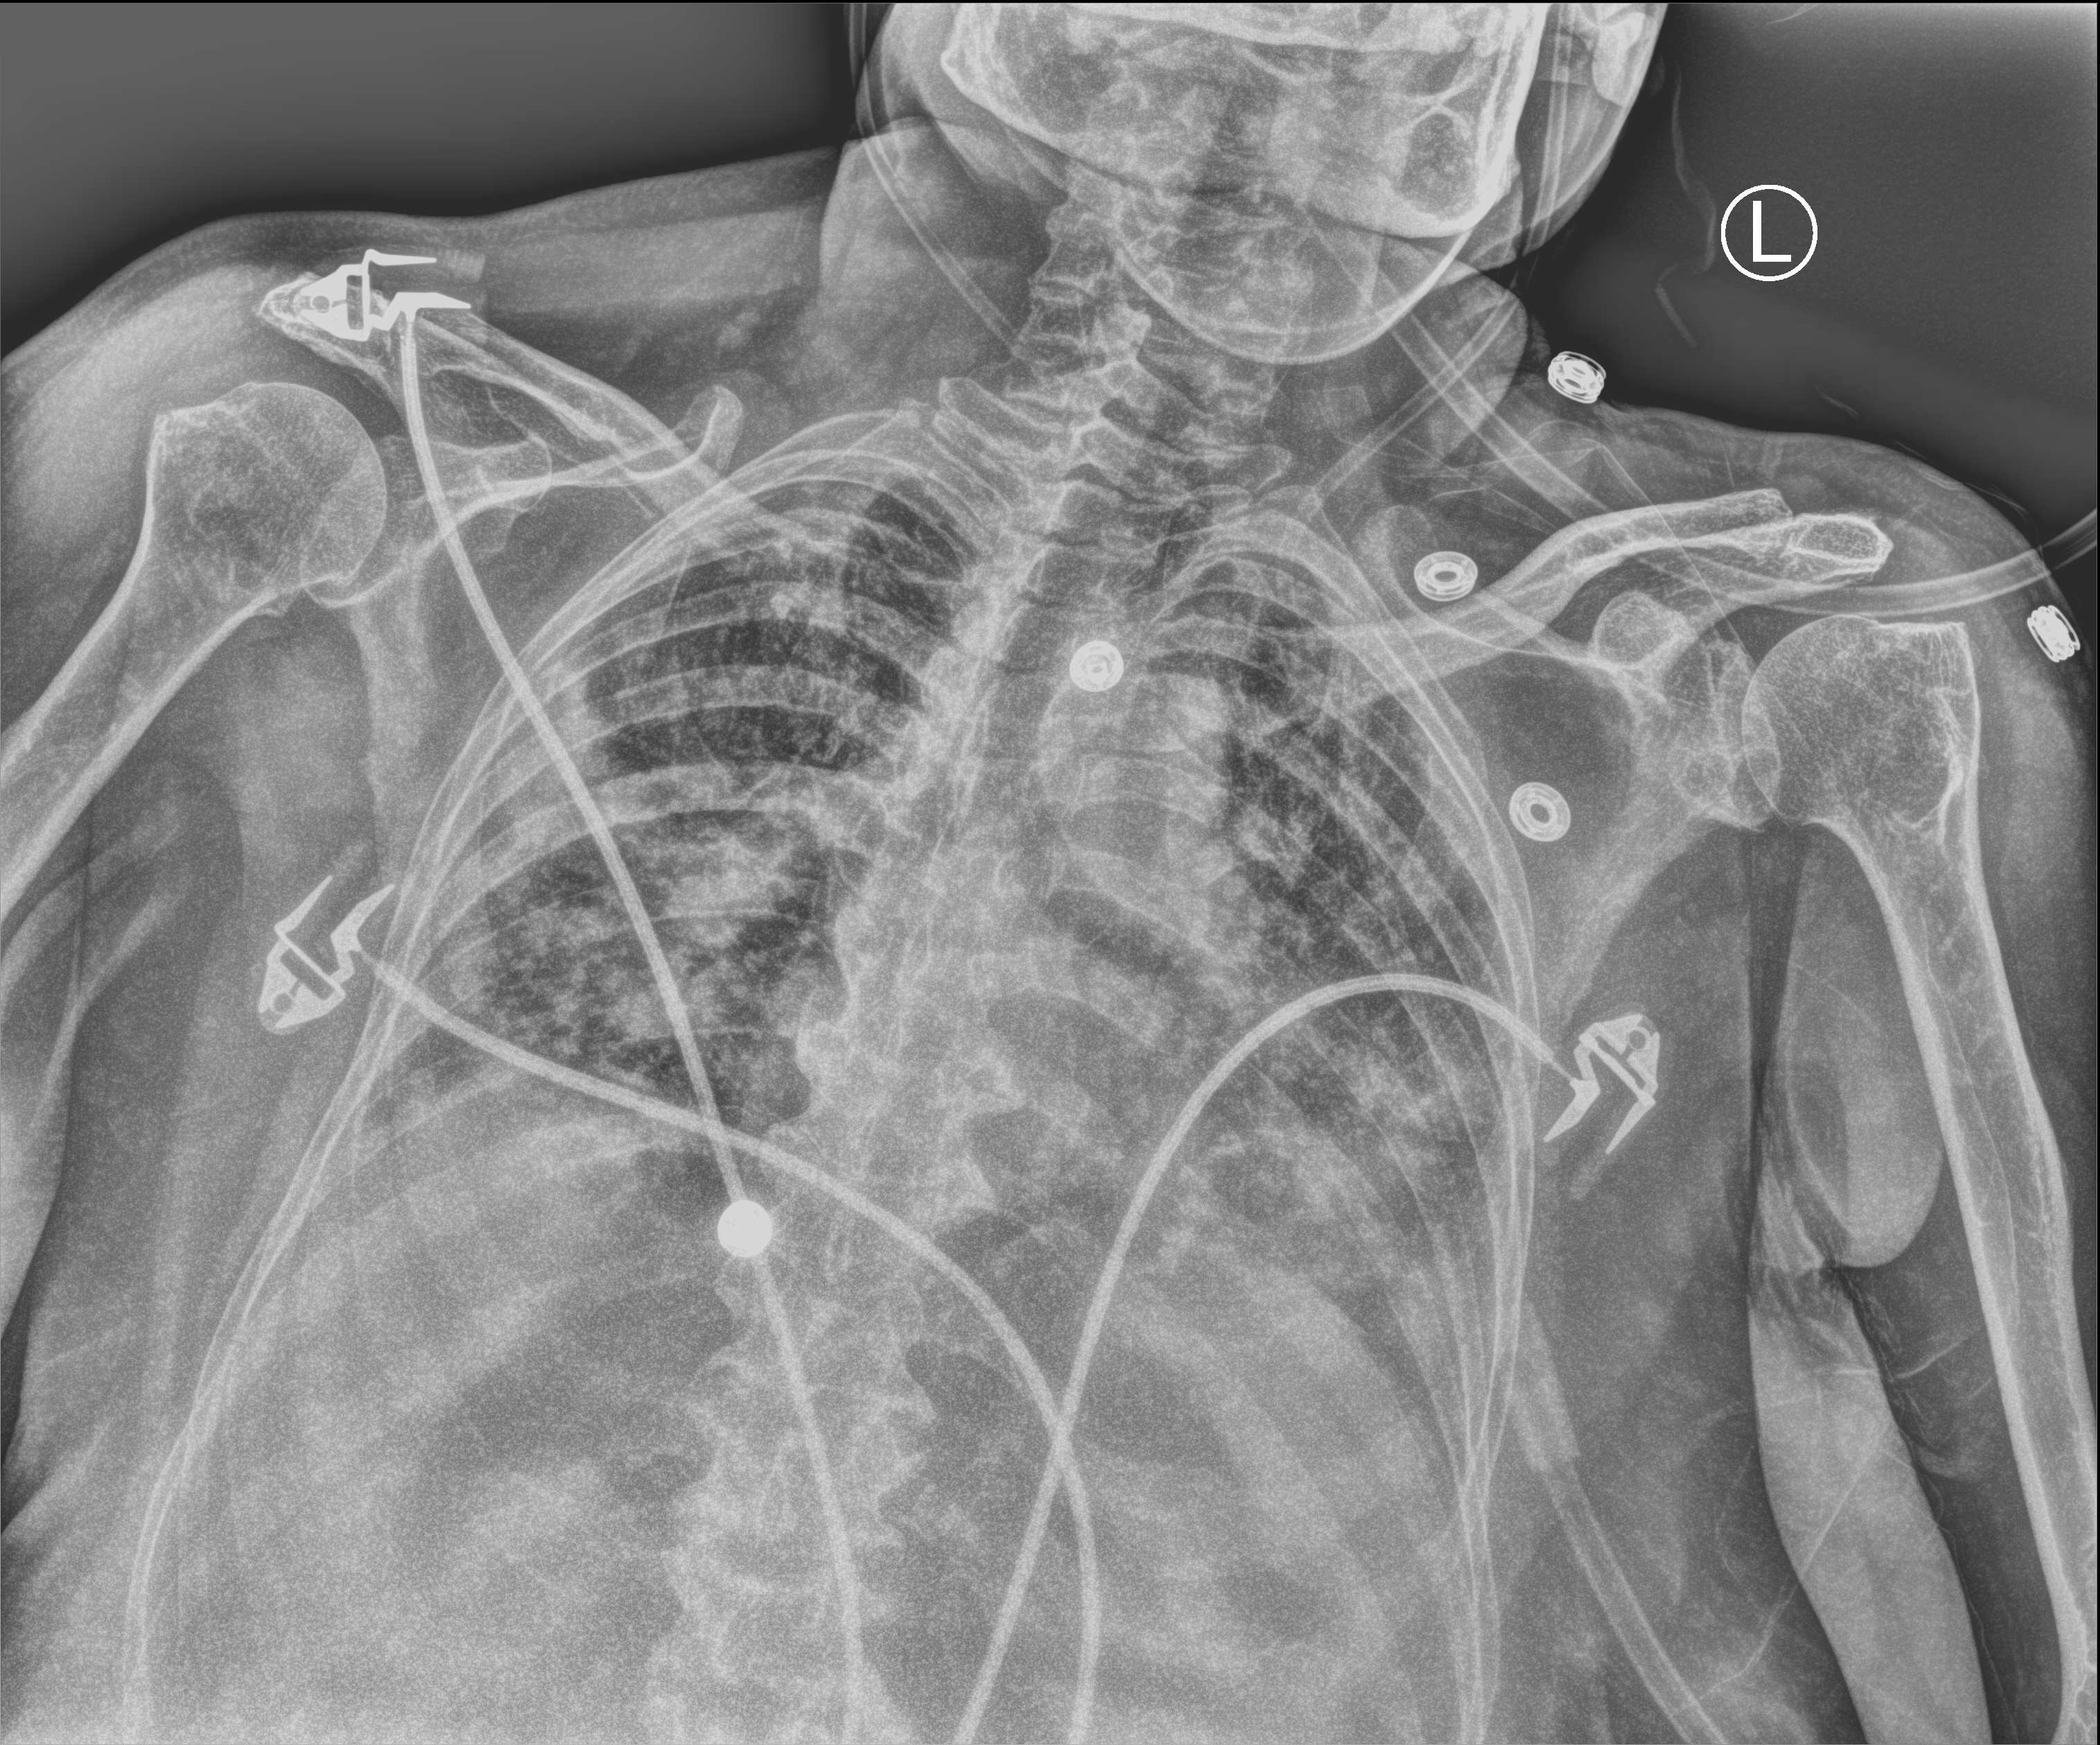
Portable chest radiograph. Female patient hospitalised with COVID-19, age 75–90 years.
Admission-level facts for this patient (not findings on this image; timing relative to this image not recorded): chronic kidney disease (admission record): no; admitted to intensive care during this hospital stay: yes.